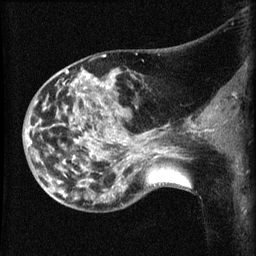
Breast MRI (dynamic contrast-enhanced), one sagittal slice. Position 25 of 60 along the scan axis. Dynamic contrast-enhanced series, image 2 of 3 at this slice position (ordered by acquisition). 1.5 T. TE 4.2 ms, TR 8.2 ms. 2.1 mm slice thickness. 256 × 256 image matrix, field of view 180 × 180 mm. Female patient, age 50 years.
Structures marked on this image (semi-automatically segmented with operator editing):
- analysis volume of interest (the breast-tissue region the enhancement analysis was run in; not a lesion): bounding box [x1, y1, x2, y2] px = [38, 72, 169, 211]
- tumour enhancement mask (voxels above the 70 % enhancement threshold inside the analysis volume of interest): [67, 72, 157, 158]